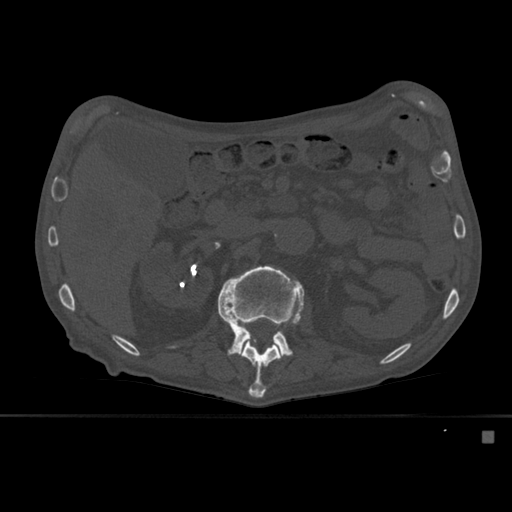
CT including the spine, one axial slice; slice 245 of 527 in the series (ordered by position); bone window (W 1800 / L 400 HU); 1.5 mm slice thickness; 512 × 512 image matrix, field of view 373 × 373 mm. Patient: male, 78 years. Case-level facts recorded for this patient, not image findings: primary cancer: prostate.
Annotated regions visible in this slice (semi-automatic segmentation, software-assisted and operator-edited):
- L1 vertebra: bounding box [x1, y1, x2, y2] px = [240, 324, 281, 398]
- L2 vertebra: [218, 265, 306, 358]